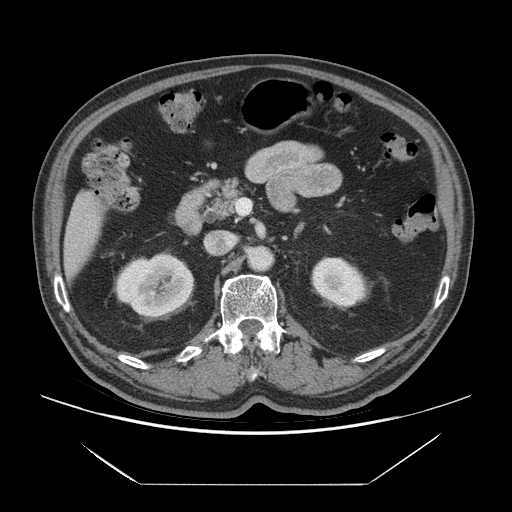
Contrast-enhanced abdominal CT (liver protocol), one axial slice. Slice 26 of 75 in the series (ordered by position). 140 kVp. Soft-tissue window (W 400 / L 40 HU). 2.5 mm slice thickness. 512 × 512 image matrix, field of view 420 × 420 mm. From the clinical record (not read from this slice): diagnosis: hepatocellular carcinoma (patient treated with transarterial chemoembolisation; whether this scan precedes or follows treatment is not stated here); TNM stage (as recorded): Stage-I; Child-Pugh class: A; tumour differentiation: well differentiated; tumour size: 5.8 cm.
Annotated regions visible in this slice (semi-automatic segmentation, software-assisted and operator-edited):
- liver parenchyma outside the tumour (the mass and vessels are separate outlines, so this box may not span the whole liver): bounding box <64,192,100,279> (left, top, right, bottom; pixels)